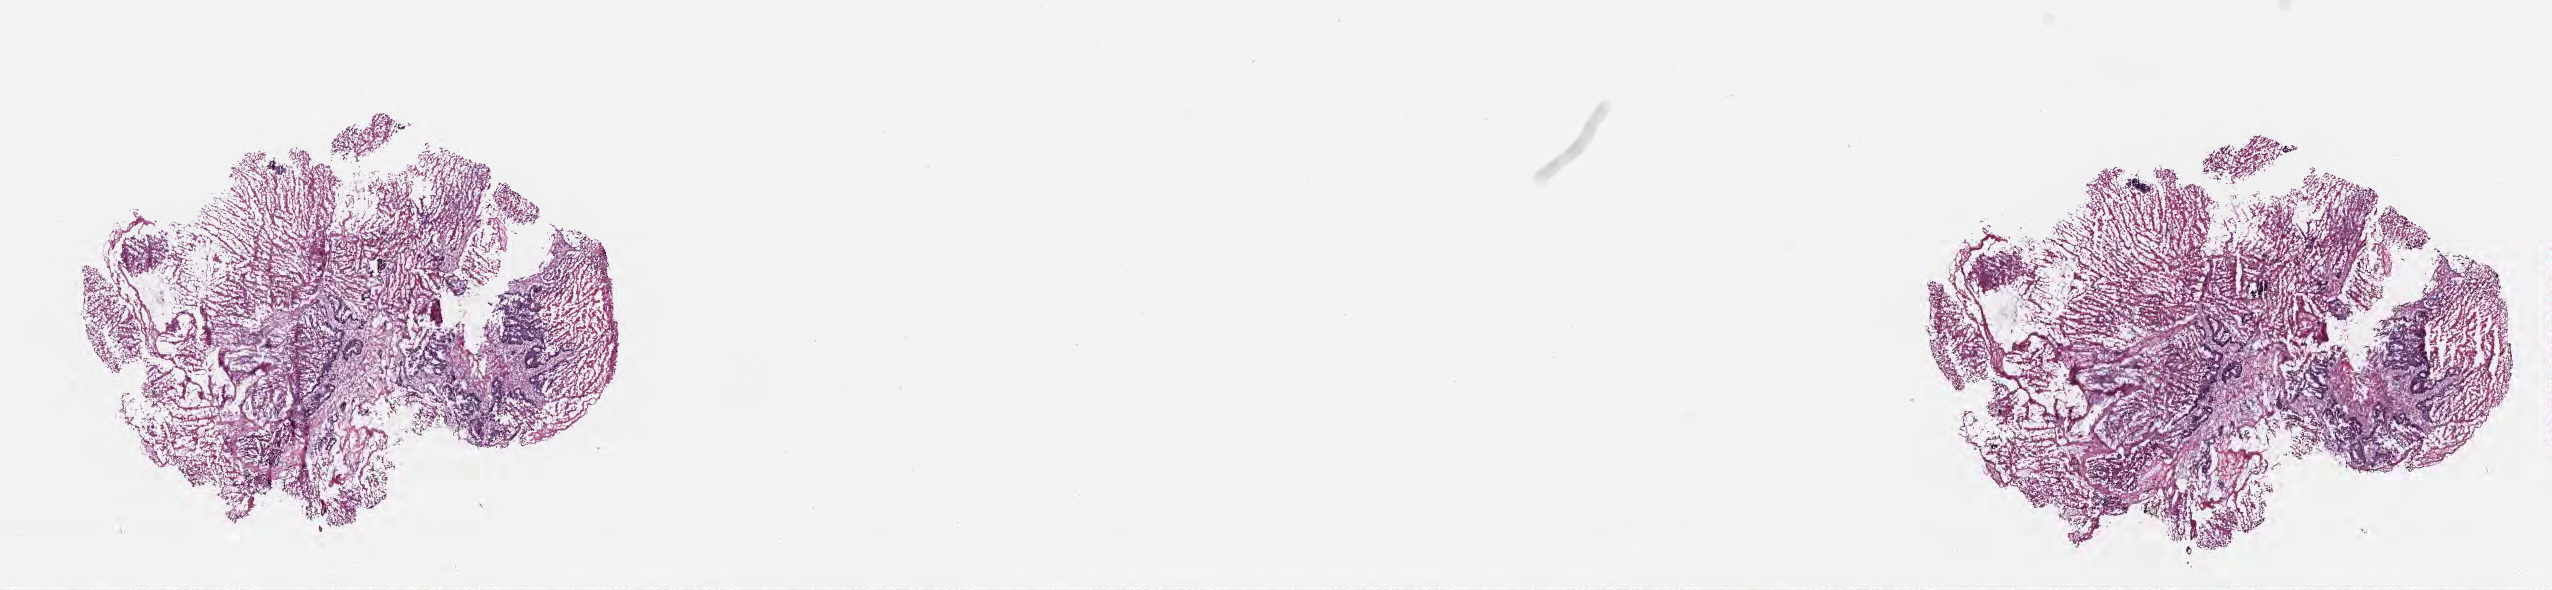
Haematoxylin and eosin whole-slide image, a low-resolution overview of the entire scanned area, about 20.6 x 4.8 mm; frozen section; specimen: metastatic tumor tissue, resected from pelvis. Female, age 66 years at initial diagnosis. Slide review estimates, as recorded: tumor cells 20%, tumor nuclei 50%, stromal cells 15%, necrosis 60%, normal cells 5%. Inflammatory infiltration, as recorded: lymphocyte infiltration 2%, monocyte infiltration 0%, neutrophil infiltration 3%.
Patient diagnosis (primary): Adenocarcinoma, metastatic, NOS. Section: bottom of the tissue portion.